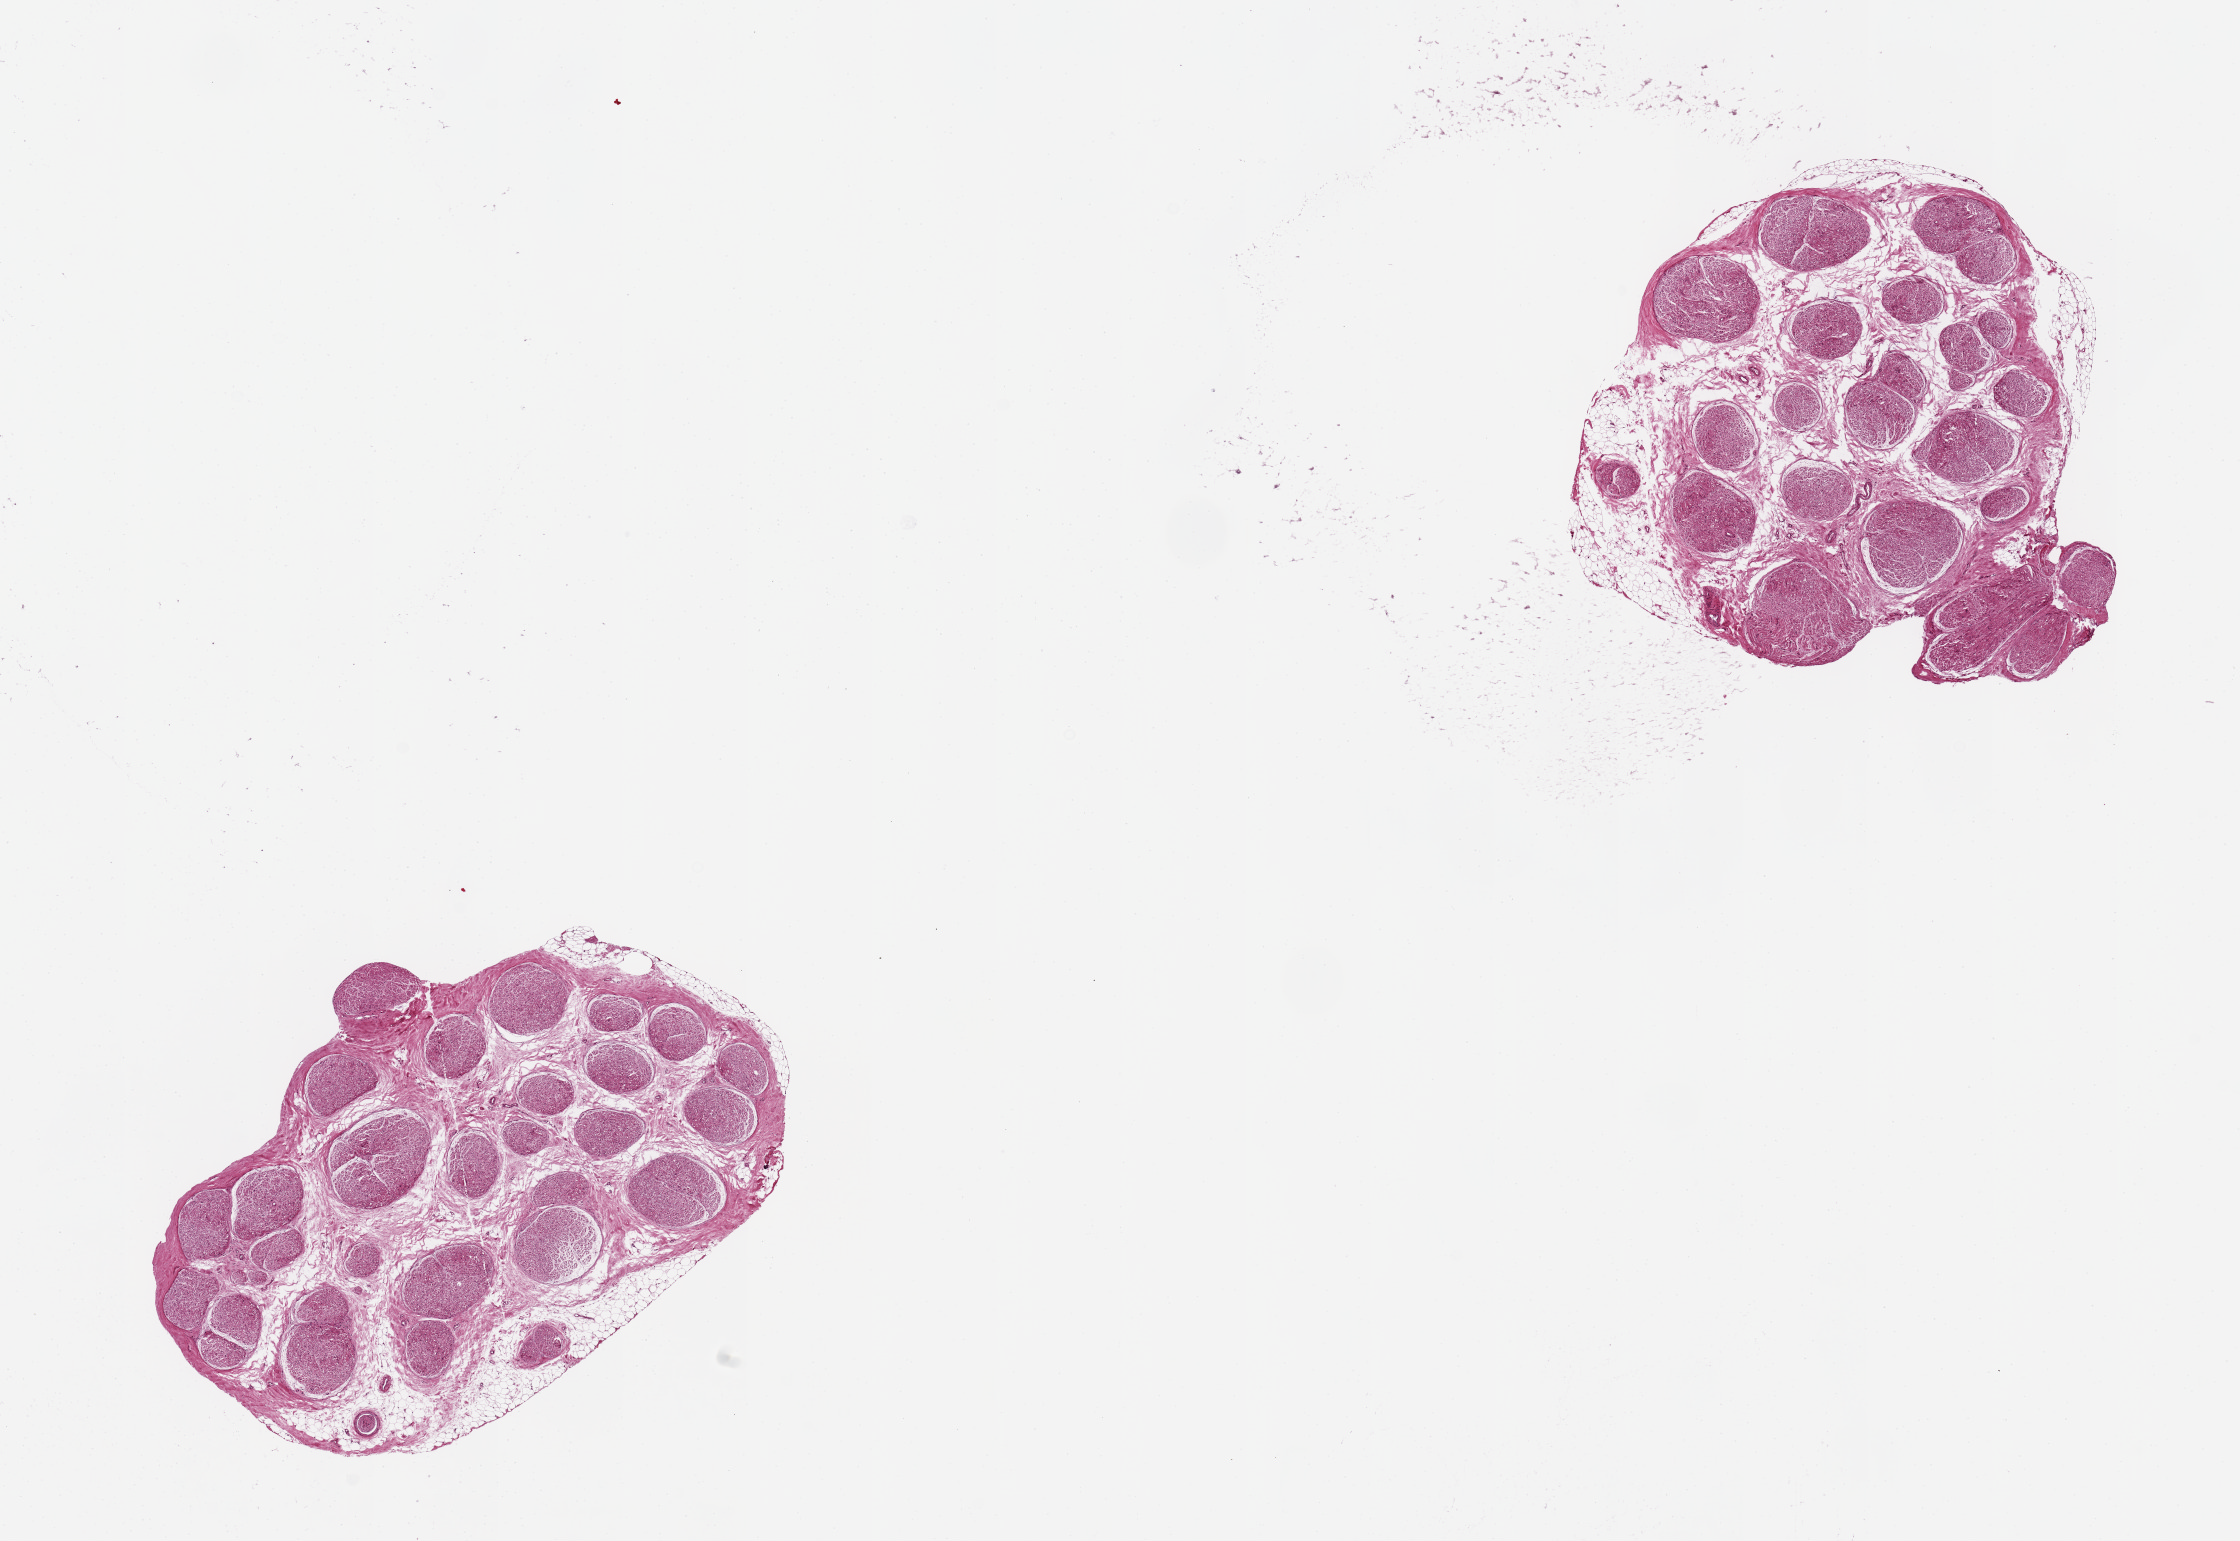
Whole-slide image, hematoxylin and eosin (H&E) stain, brightfield — low-resolution overview of the scanned area, about 17.7 x 12.2 mm (acquisition: 20x scan), PAXgene-fixed, paraffin-embedded tissue, sampled site (target tissue): tibial nerve, tissue donor sample. Female donor.
Reviewer comment on this tissue sample: 2 pieces, 4.4 and 4.9 mm fat/connective tissue, nerve is~25% of total specimen.